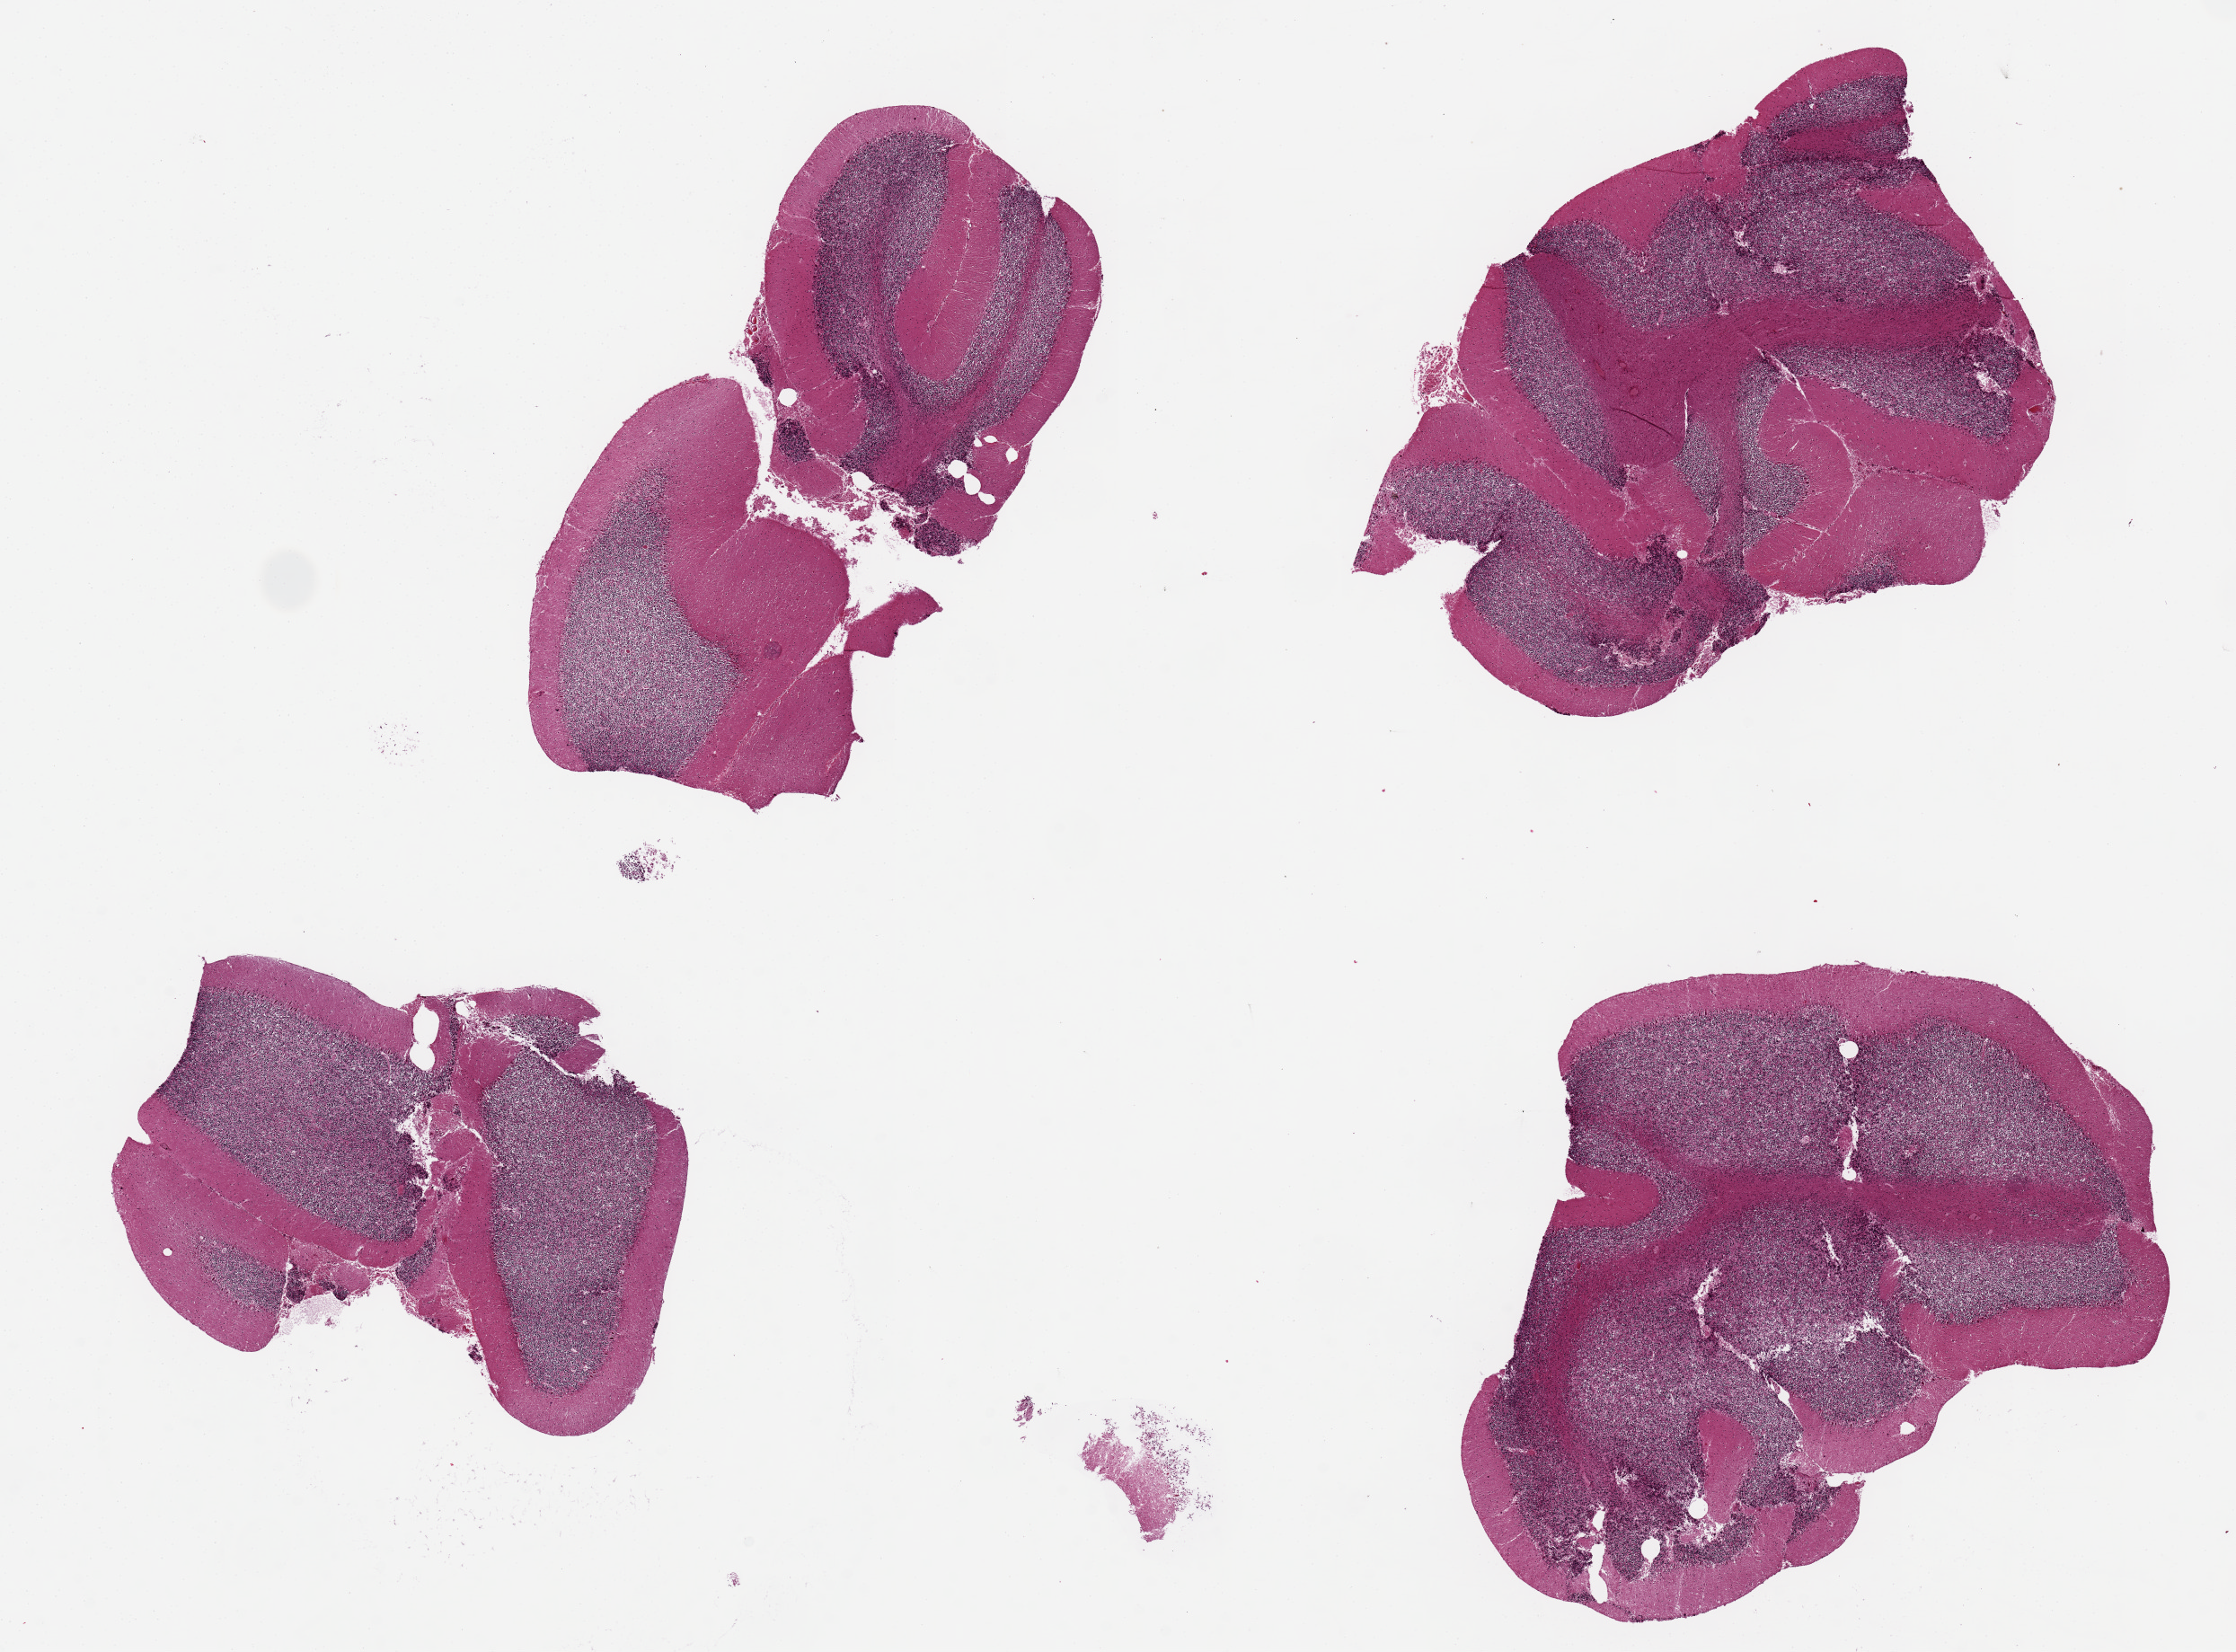
Digitized hematoxylin and eosin (H&E)-stained section, brightfield, shown as a low-resolution overview of the whole scanned area (about 19.7 x 14.5 mm); PAXgene-fixed, paraffin-embedded tissue; section of cerebellum (target tissue); tissue donor sample.
- pathologist's review note for this sample: 4 pieces, ~6x6mm